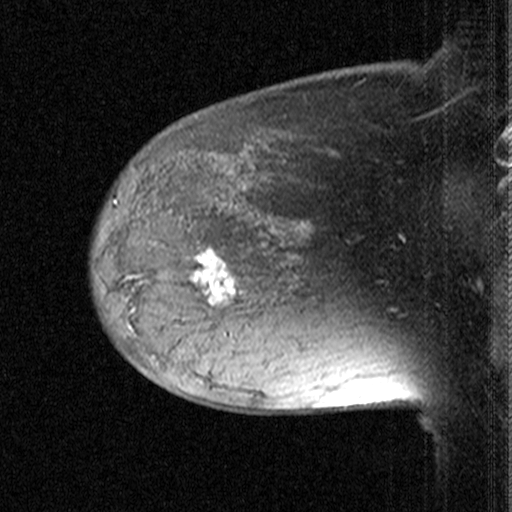
Breast MRI (dynamic contrast-enhanced), one sagittal slice. Dynamic contrast-enhanced study with each time point stored as its own series, time point 2 of 3 at this slice position (early post-contrast, ordered by acquisition time). 1.5 T. TE 4.5 ms, TR 11 ms. 3 mm slice thickness. 512 × 512 image matrix, field of view 200 × 200 mm. Patient: female, 38 years. From the clinical record (not read from this slice): setting: breast cancer imaged before/during neoadjuvant chemotherapy; receptor status: HR-positive, HER2-negative.
Outlined on this slice (semi-automatic segmentation, software-assisted and operator-edited):
- analysis volume of interest (the breast-tissue region the enhancement analysis was run in; not a lesion): box from (x=170, y=232) to (x=259, y=331) px
- tumour enhancement mask (voxels above the 90 % enhancement threshold inside the analysis volume of interest): (x=194, y=249)–(x=235, y=305)